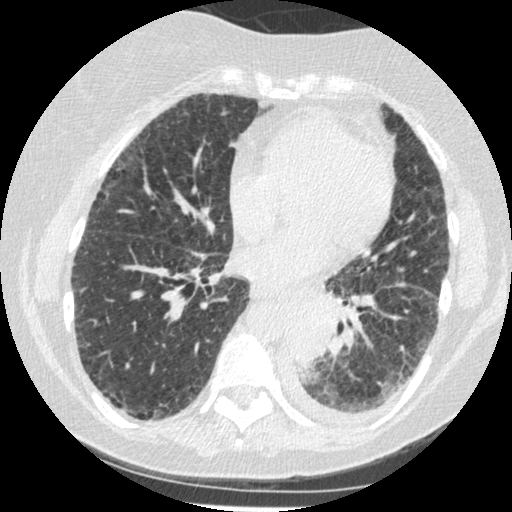
Axial slice from a low-dose chest CT screening exam. Third screening round (two years after baseline). Lung window (W 1500 / L -600 HU). Slice 249 of 341 in the series. 512 × 512 image matrix. Female participant, aged 60 years at enrolment. Former smoker at enrolment.
- Expert reader's lesion annotation, box from (x=277, y=302) to (x=343, y=376) px.
- Screening reader's record for this exam (one nodule recorded; not confirmed to be the boxed lesion): non-calcified nodule or mass ≥4 mm, left lower lobe, 54 × 38 mm, smooth margins, soft tissue attenuation, pre-existing on the prior screen: yes; interval growth: yes.
- Lung cancer was diagnosed 15 days after this screen: small cell carcinoma, NOS, left lower lobe, undifferentiated (G4), stage IV (AJCC 6th edition), 69 mm at pathology.